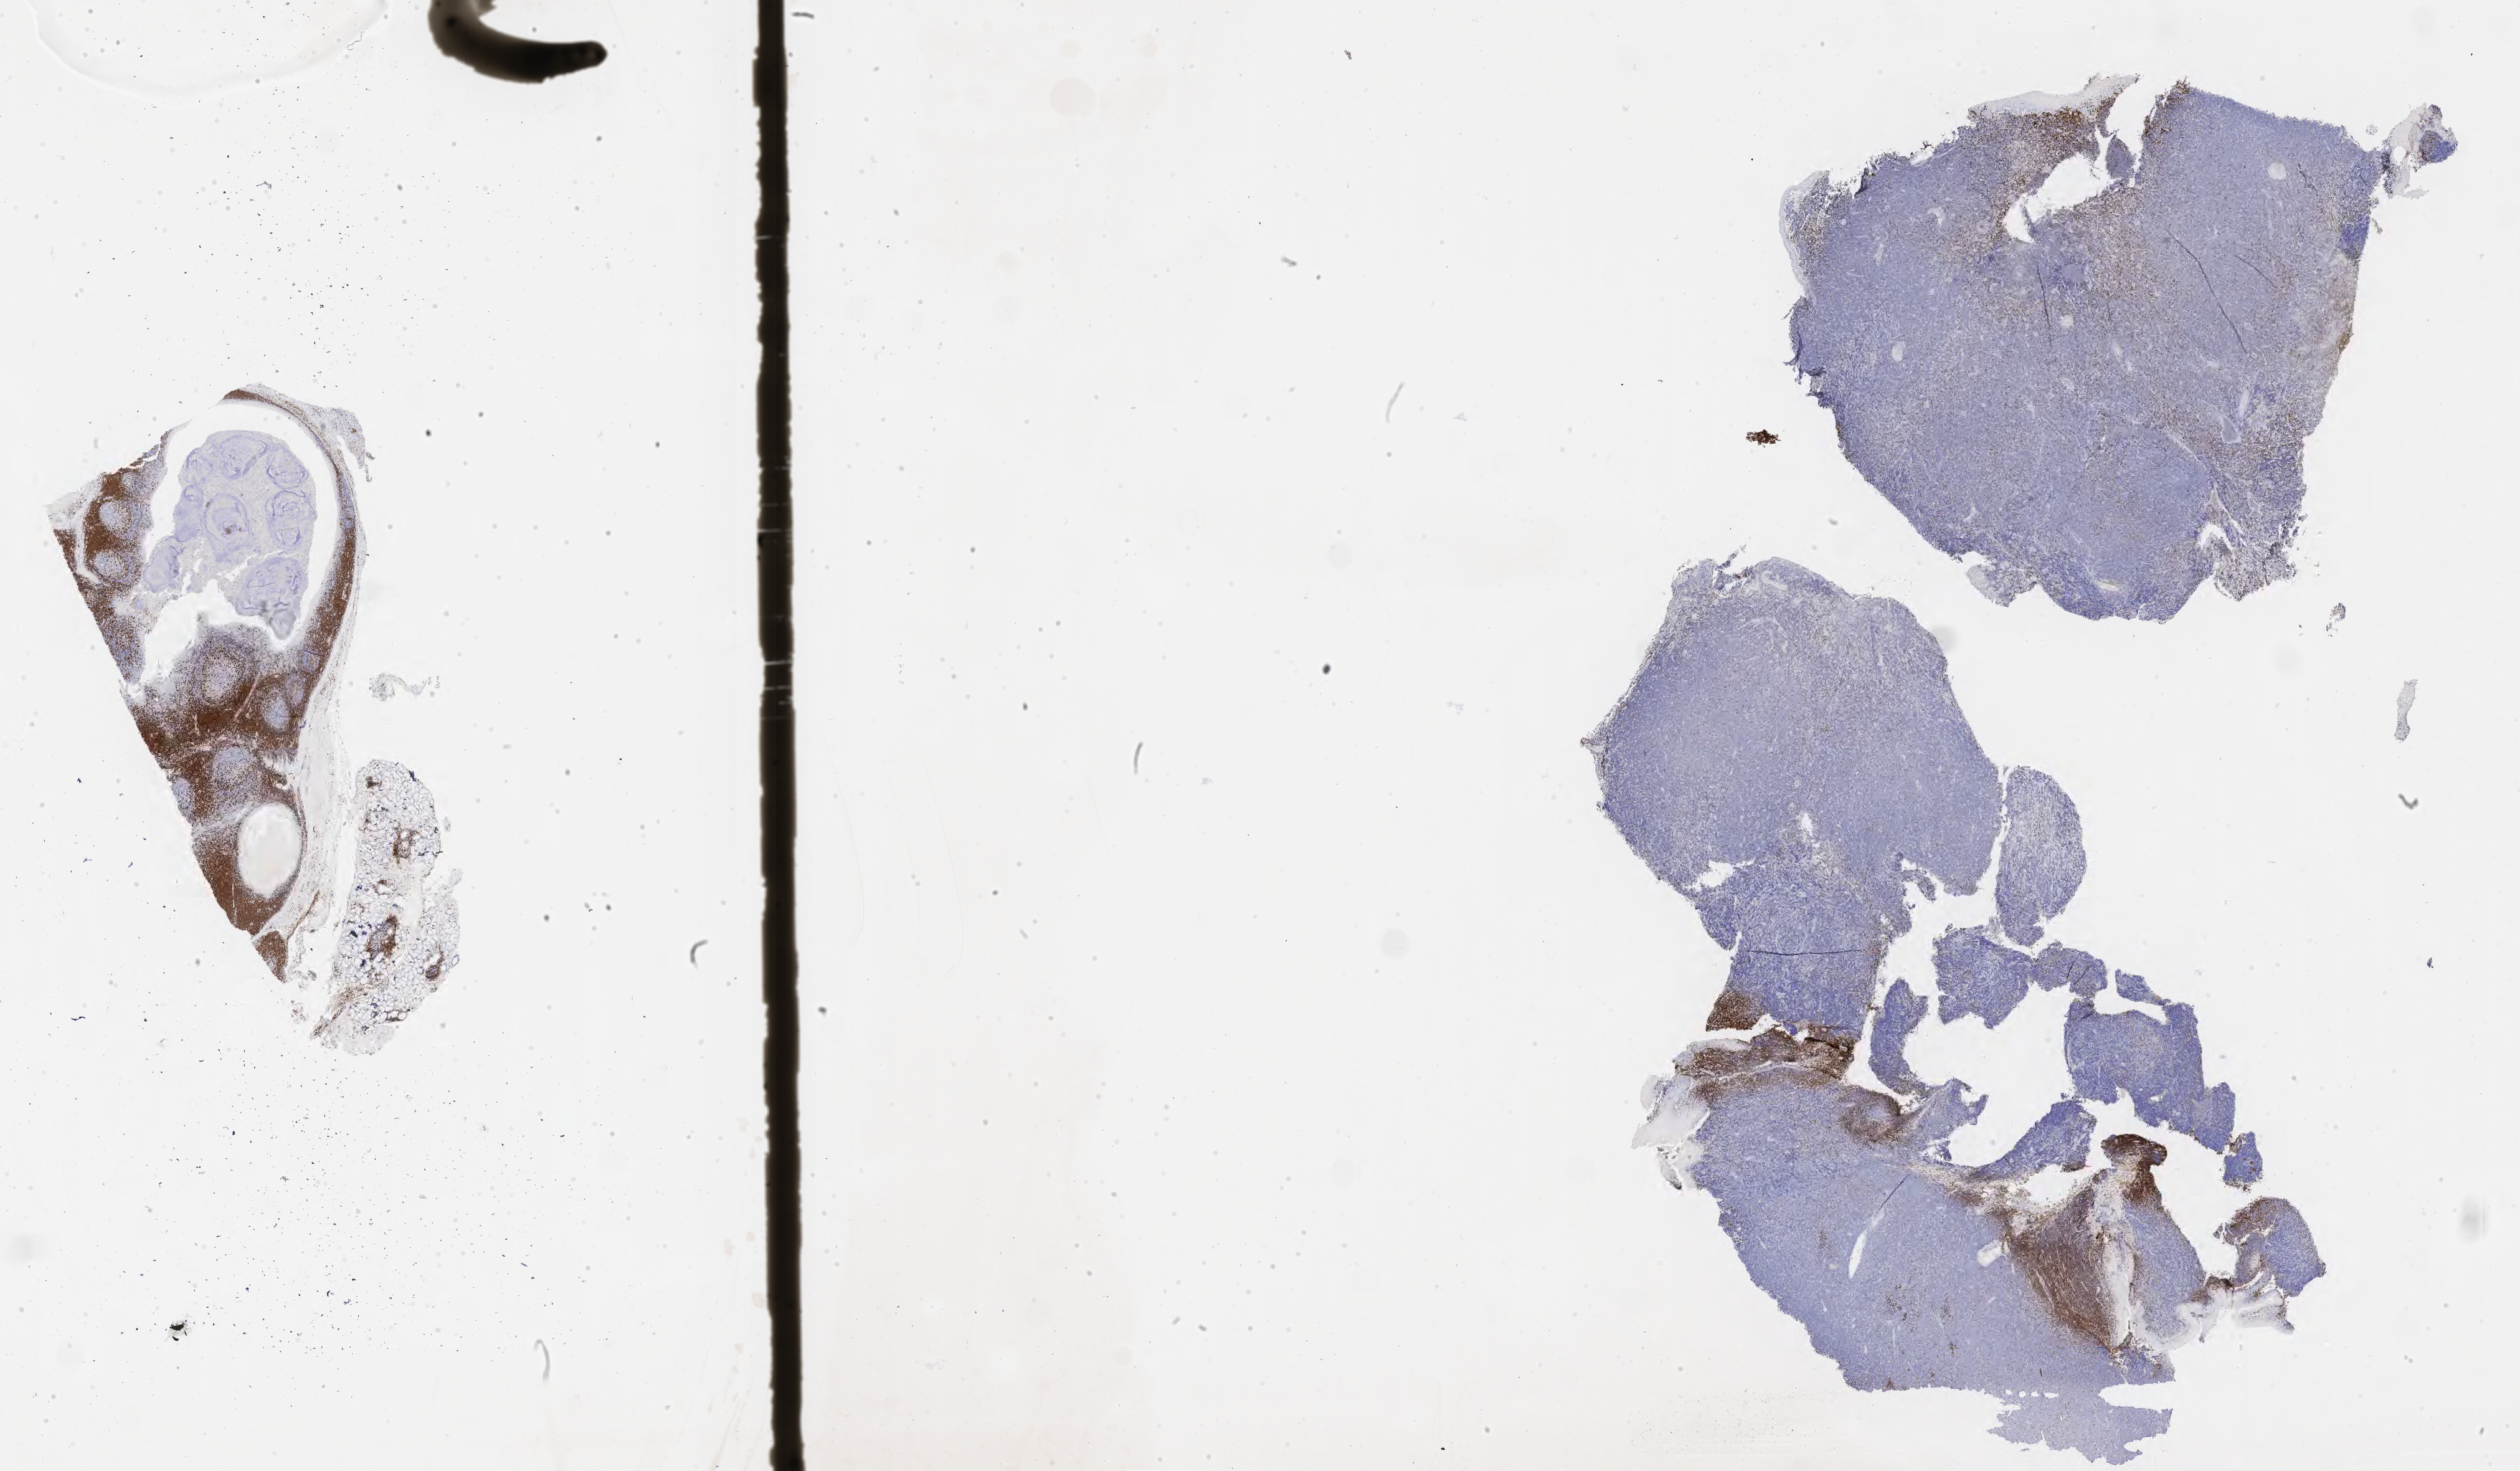
IHC for CD3, whole-slide image, whole scanned area (about 32.7 x 19.1 mm) shown as a low-resolution overview. Specimen: tumor tissue. Male patient, aged 22.
Diagnosis: Diffuse large B-cell lymphoma, NOS.